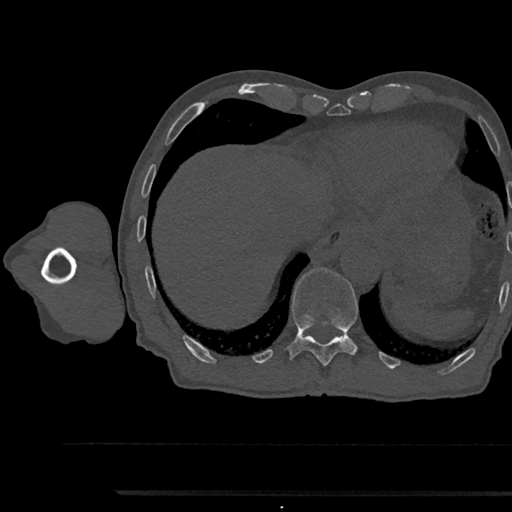
CT including the spine, one axial slice. Position 785 of 797 along the scan axis. Reconstruction kernel Br40s/3. 120 kVp. Bone window (W 1800 / L 400 HU). 0.5 mm slice thickness. 512 × 512 image matrix, field of view 367 × 367 mm. Male patient, age 79 years. Case-level facts recorded for this patient, not image findings: primary cancer: prostate.
Outlined on this slice (semi-automatically segmented with operator editing):
- T11 vertebra: bounding box <288,267,358,367> (left, top, right, bottom; pixels)